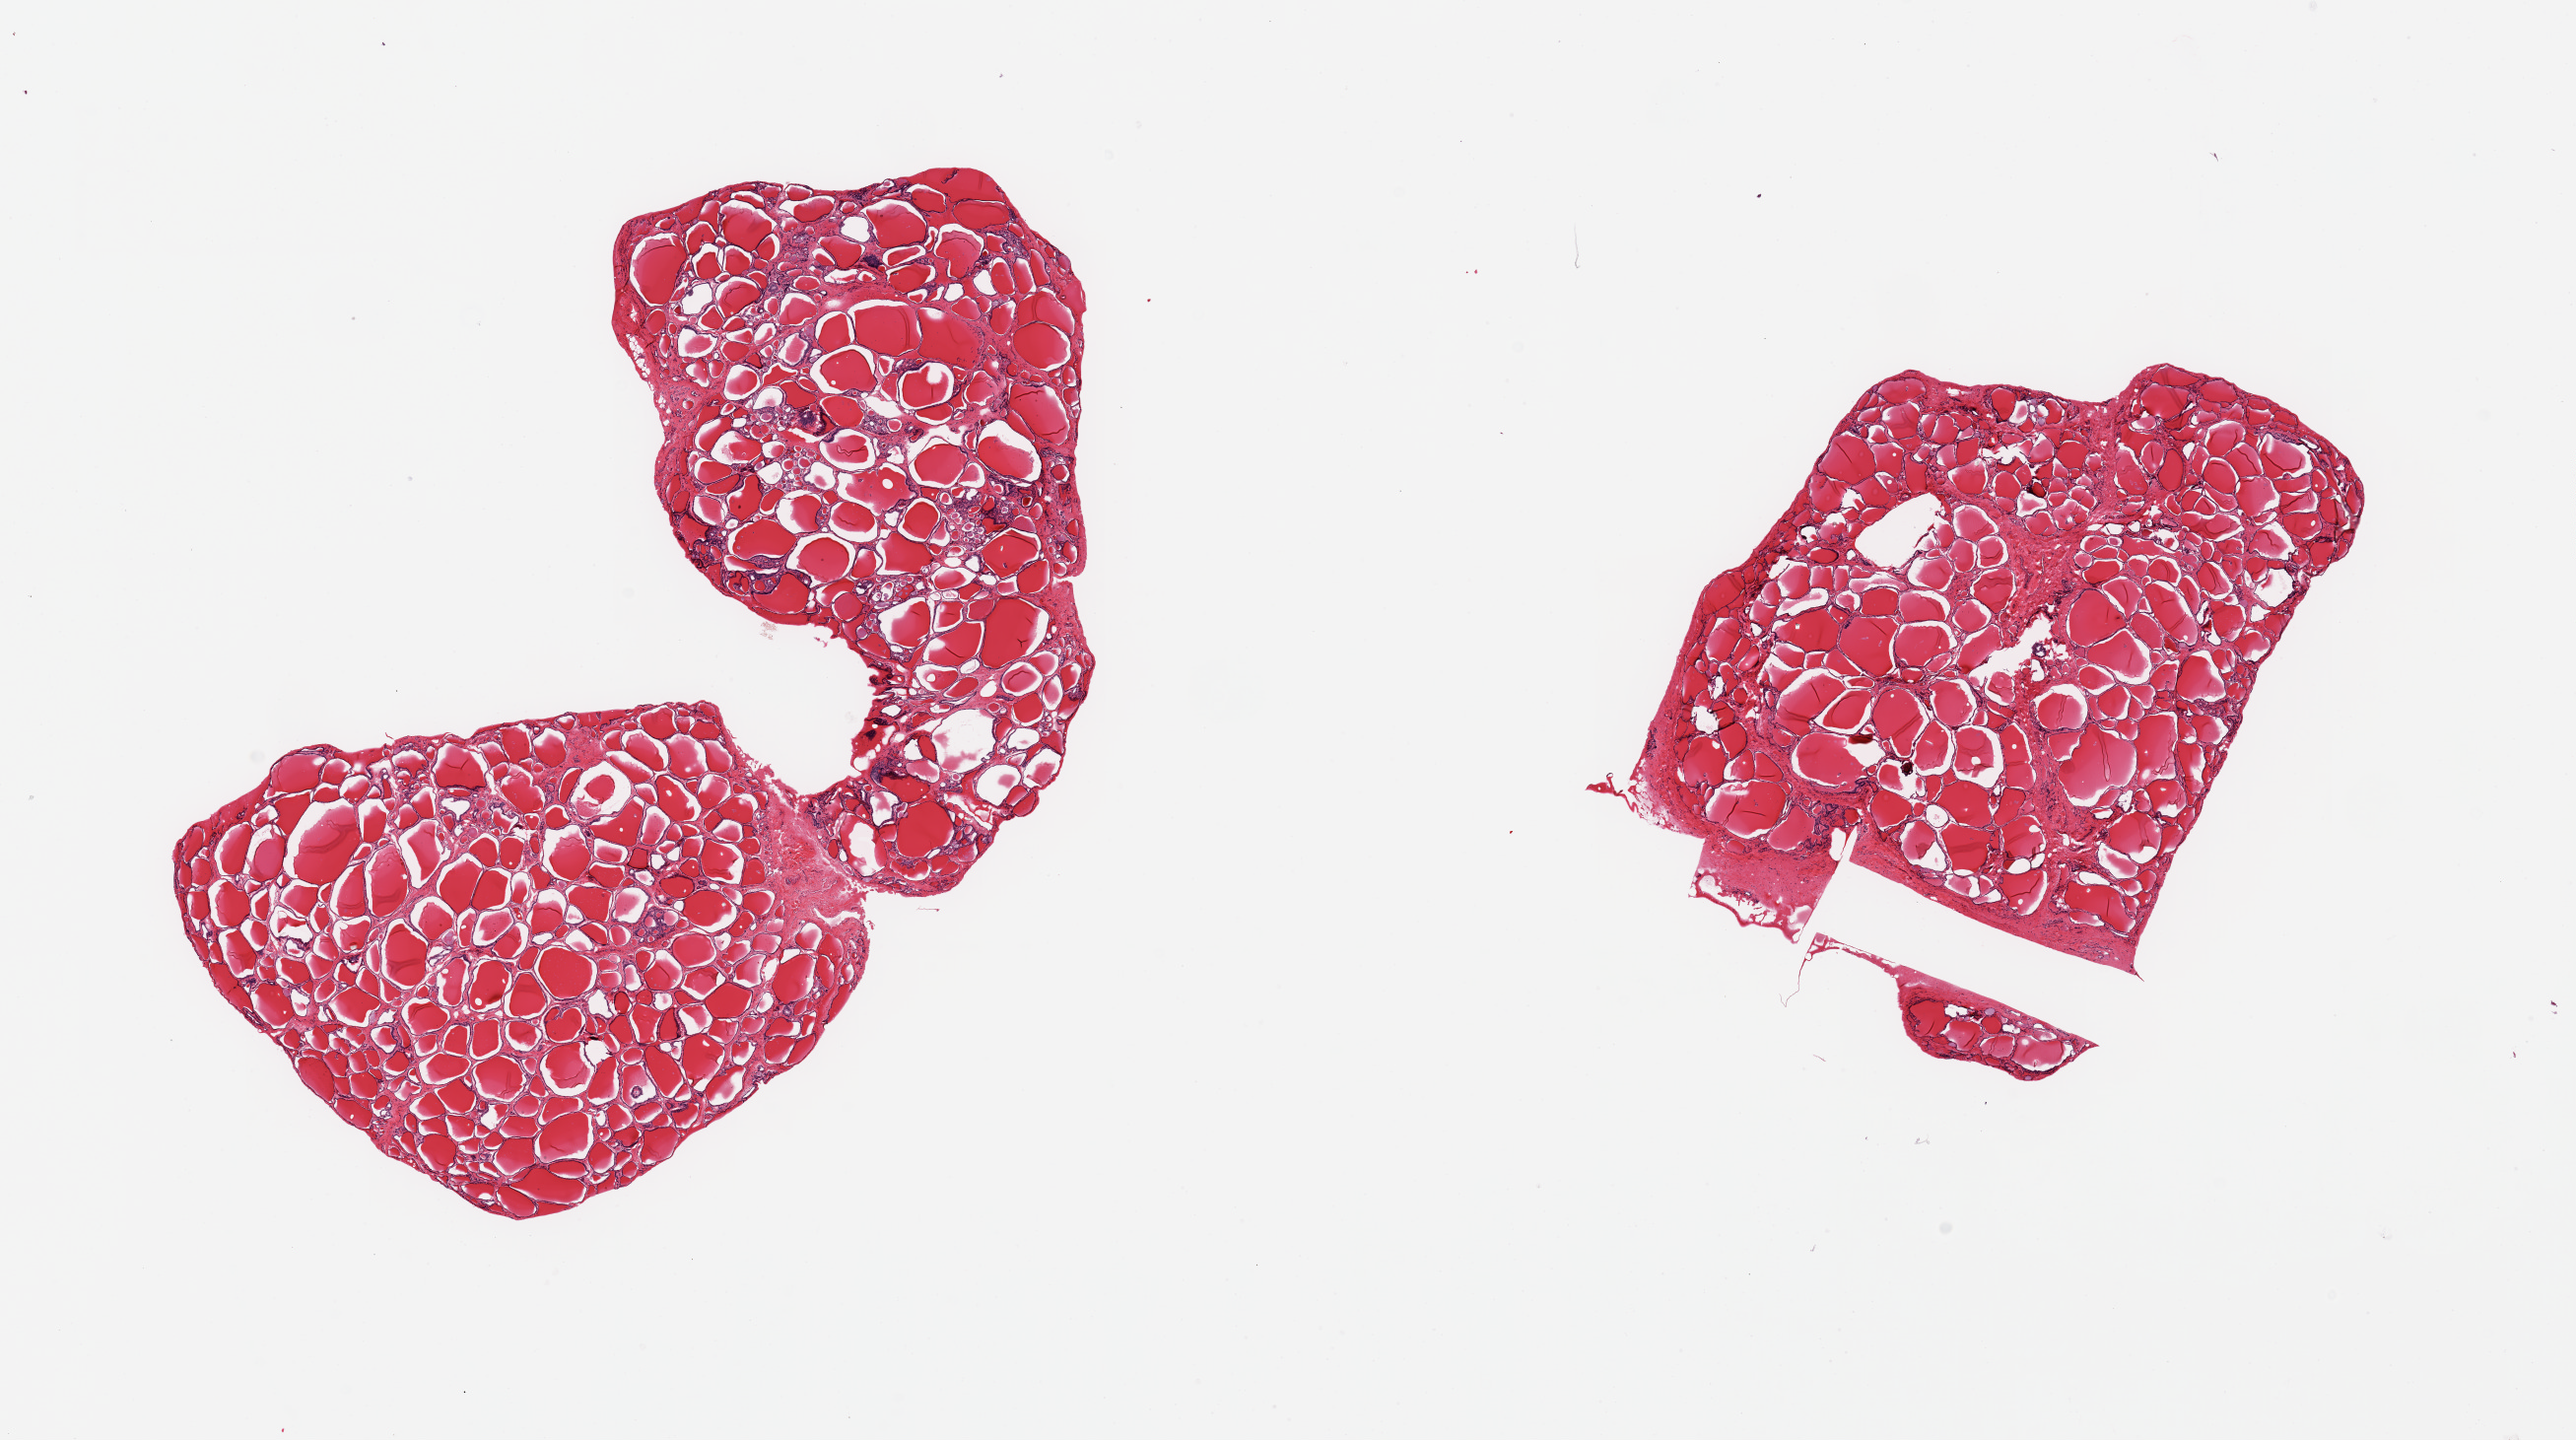
H&E whole-slide image — whole scanned area (about 20.7 x 11.6 mm) shown as a low-resolution overview; PAXgene-fixed paraffin-embedded (PFPE) section; section of thyroid (target tissue); tissue donor sample. Donor: male.
Review note (as recorded): 2 pieces, no signficant abnormalities.